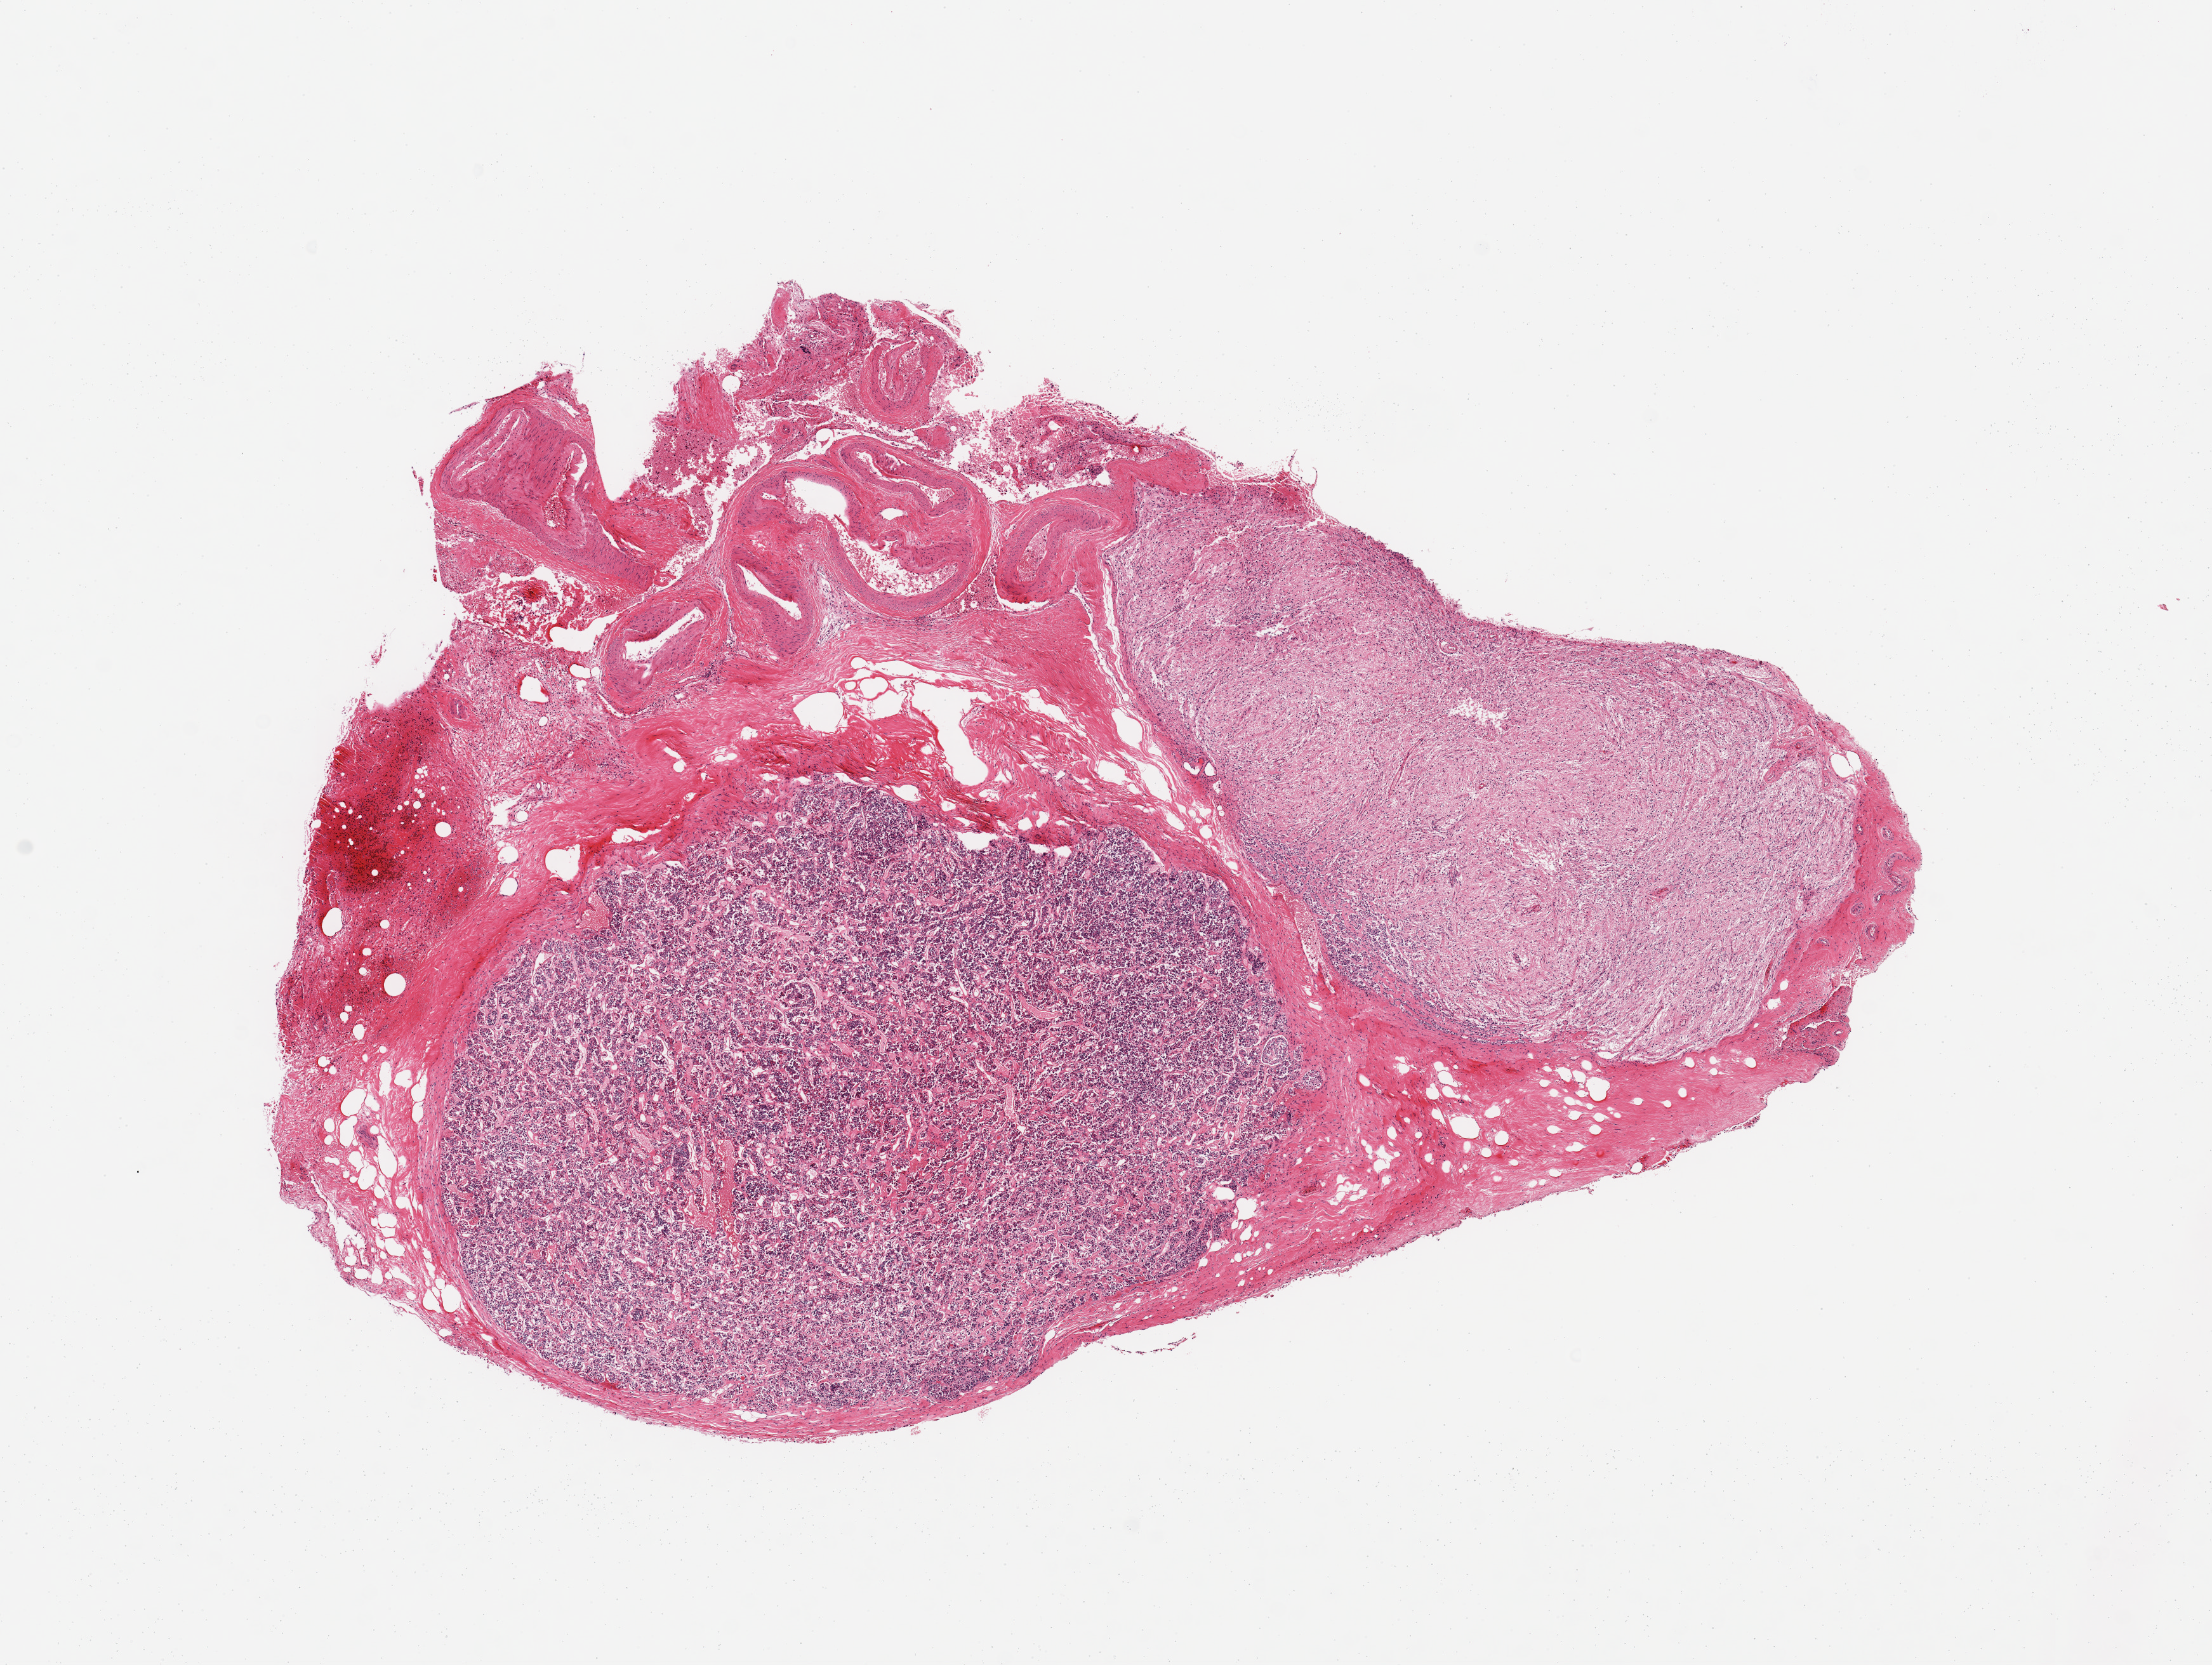
Digitized H&E-stained section — a low-resolution overview of the entire scanned area, about 13.8 x 10.4 mm (slide scanned at 20x). PAXgene-fixed, paraffin-embedded tissue. Sampled site (target tissue): pituitary. Donor tissue sample.
Review note (as recorded): 1 piece; 40% adenohypophysis, 30% neurohypophysis, remainder is dura/vessels/hemorrhage.